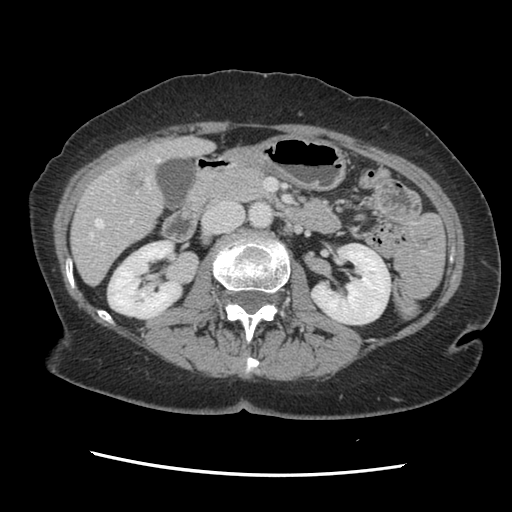
Contrast-enhanced abdominal CT, one axial slice; 120 kVp; soft-tissue window (W 400 / L 40 HU); 512 × 512 image matrix, field of view 330 × 330 mm. Female patient, age 61 years. Case-level facts recorded for this patient, not image findings: diagnosis: colorectal cancer liver metastases, imaged before liver resection; multiple liver metastases: no.
Outlined on this slice (outlined manually by an expert reader):
- hepatic veins: bounding box [x1, y1, x2, y2] px = [90, 159, 160, 238]
- liver: [72, 138, 211, 283]
- planned liver remnant (the part of the liver to remain after resection): [72, 146, 206, 283]
- portal vein (with intrahepatic branches): [102, 192, 138, 245]
- liver metastasis: [121, 168, 145, 191]